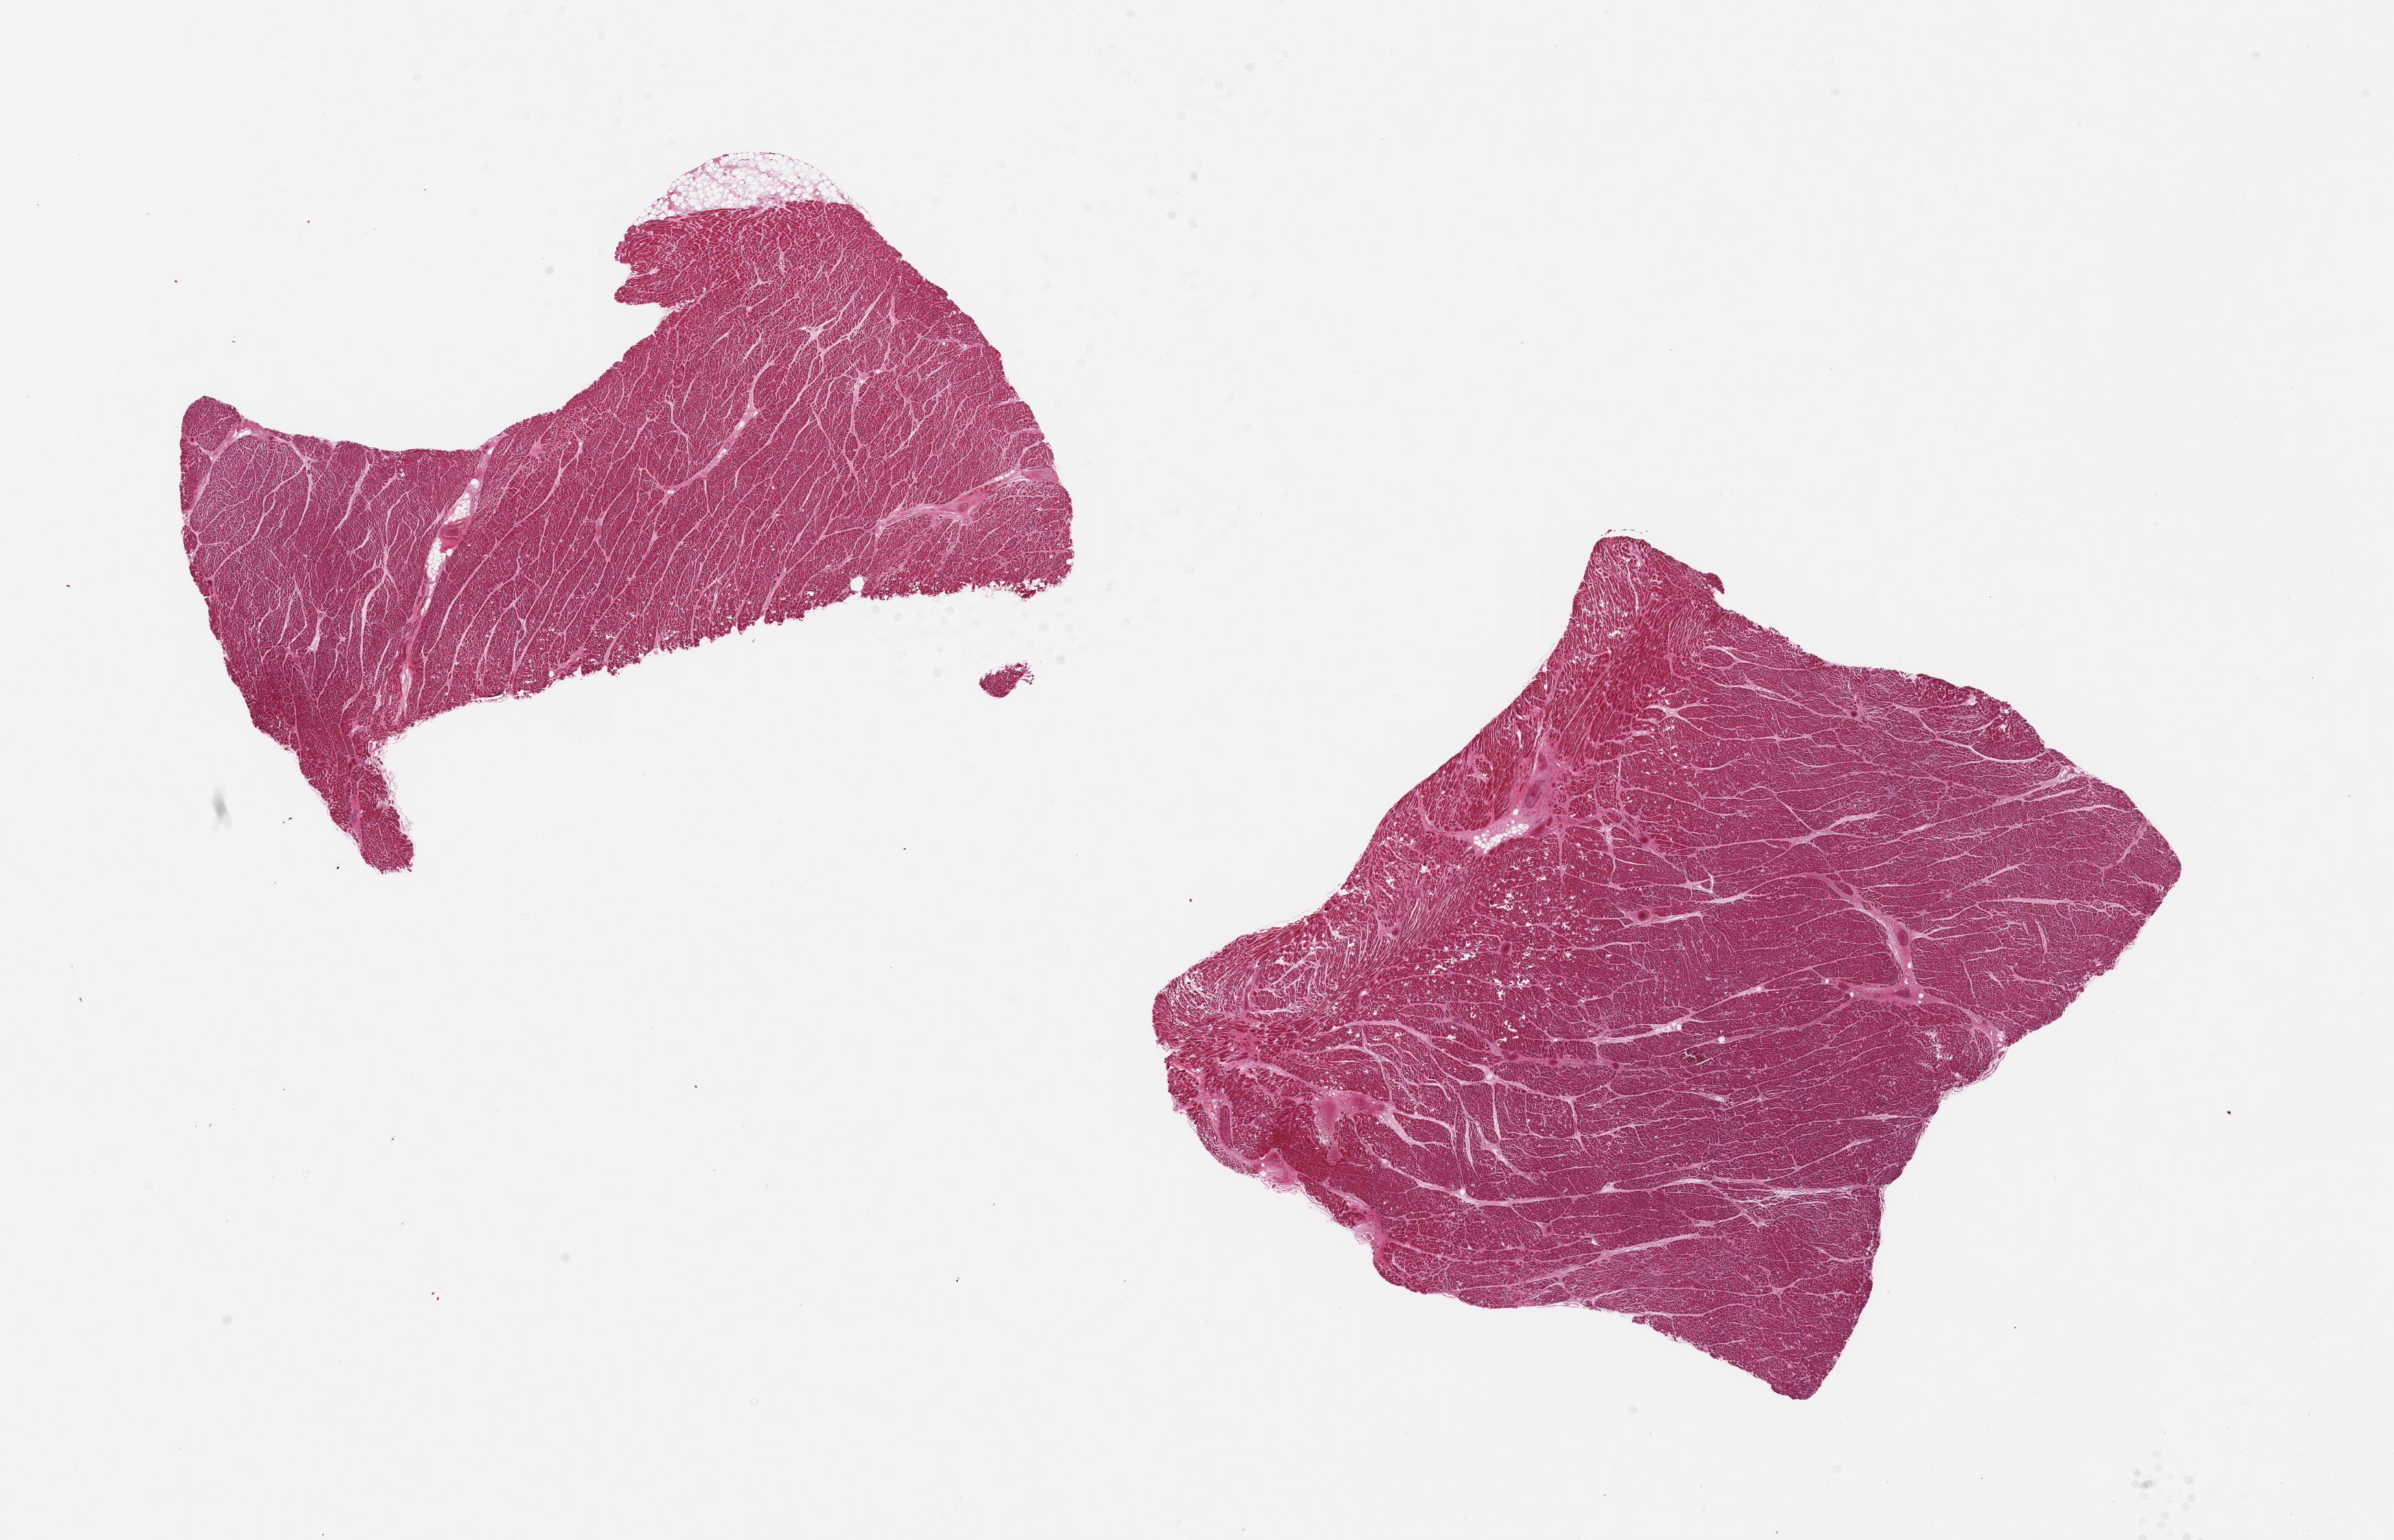
Digitized hematoxylin and eosin (H&E)-stained section — a low-resolution overview of the entire scanned area, about 27.6 x 17.7 mm. PAXgene-fixed, paraffin-embedded tissue. Section of heart (target tissue). Donor tissue sample. Donor: male.
• reviewer comment on this tissue sample: 2 pieces